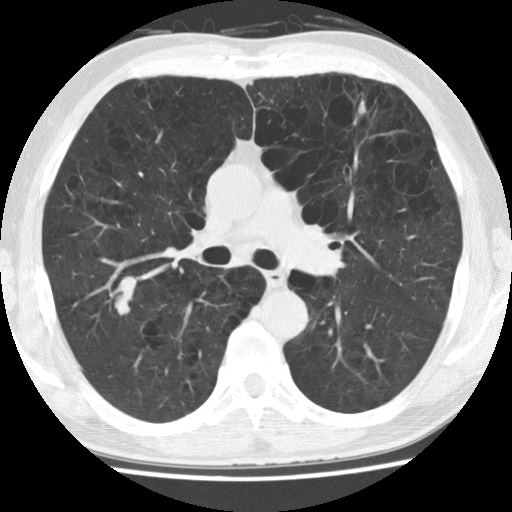
Low-dose screening chest CT, one axial slice. Slice 93 of 158 in the series (ordered by position). 120 kVp. Lung window (W 1500 / L -600 HU). 2.5 mm slice thickness. 512 × 512 image matrix.
Outlined on this slice (expert manual segmentation):
- lesion 1 (tumor, upper lobe of right lung): bounding box <115,291,133,315> (left, top, right, bottom; pixels)